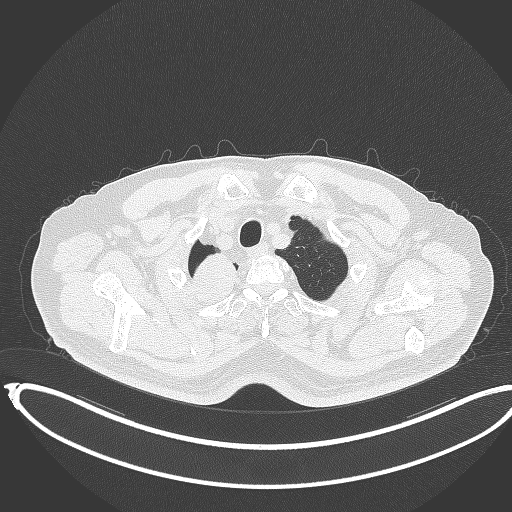
Chest CT, one axial slice; position 336 of 403 along the scan axis; reconstruction kernel B70f; lung window (W 1500 / L -600 HU); 1 mm slice thickness; 512 × 512 image matrix. Male patient, age 68 years. From the clinical record (not read from this slice): clinical TNM (as recorded): T2a N0 M0.
Structures marked on this image (rectangle marked by the reading radiologist):
- lung tumour (recorded histology: adenocarcinoma): bounding box [x1, y1, x2, y2] px = [188, 246, 248, 307]